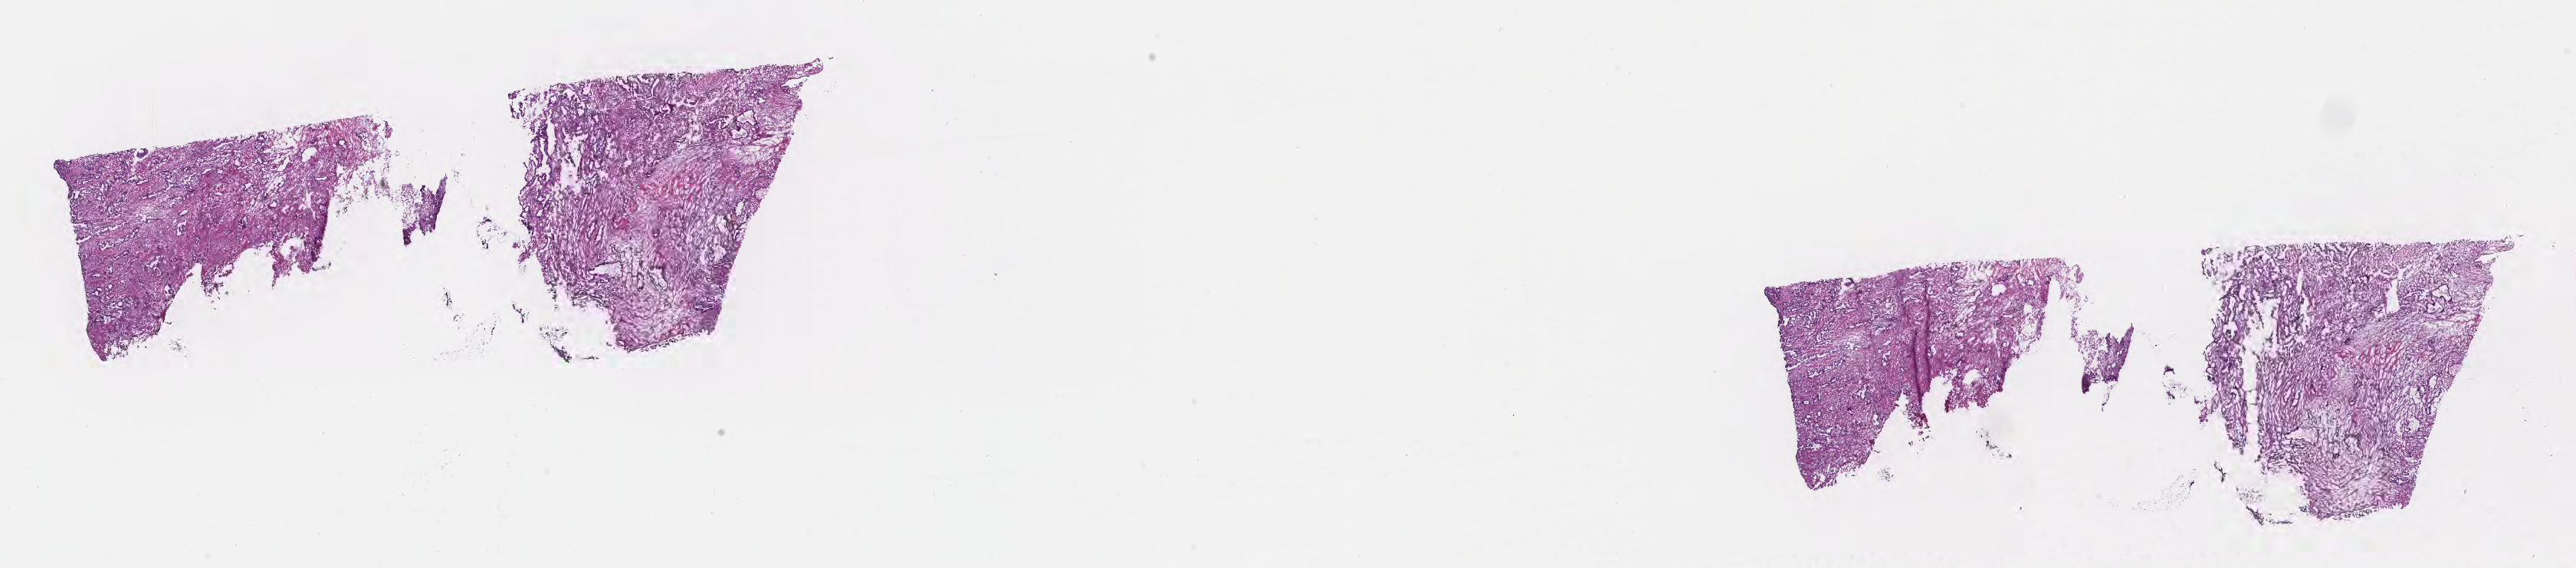
Digitized hematoxylin and eosin (H&E)-stained section — low-resolution overview of the scanned area, about 27.2 x 6.0 mm. Frozen section (tissue freezing medium). Specimen: primary tumor. Site: extrahepatic bile duct. Male patient; age at initial diagnosis 52 years. Tumor grade: G2 (moderately differentiated). Pathologist review of this section (percent, as recorded): tumor cells 60%, tumor nuclei 60%, stromal cells 30%, necrosis 0%, normal cells 10%. Inflammatory infiltration, as recorded: lymphocyte infiltration 7%, monocyte infiltration 7%, neutrophil infiltration 9%.
Diagnosis: Adenocarcinoma, NOS. Section: top of the tissue portion. AJCC pathologic stage: Stage IIIA.